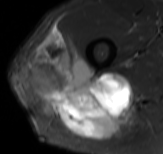
MRI of an extremity soft-tissue mass, one axial slice; position 55 of 61 along the scan axis; STIR; MR volume resampled by the dataset authors to the PET/CT grid (not the native acquisition matrix); 3.27 mm slice thickness; 163 × 154 image matrix, field of view 159 × 150 mm. Male patient. Case-level facts recorded for this patient, not image findings: histological type: poorly differentiated synovial sarcoma; grade: high; site of the primary tumour: right buttock.
Annotated regions visible in this slice (expert contour drawn on MRI and transferred to this co-registered scan by the dataset authors):
- gross tumour volume including surrounding oedema: bounding box (x1, y1, x2, y2) in pixels: (23, 27, 145, 140)
- gross tumour volume (mass): (23, 27, 131, 140)